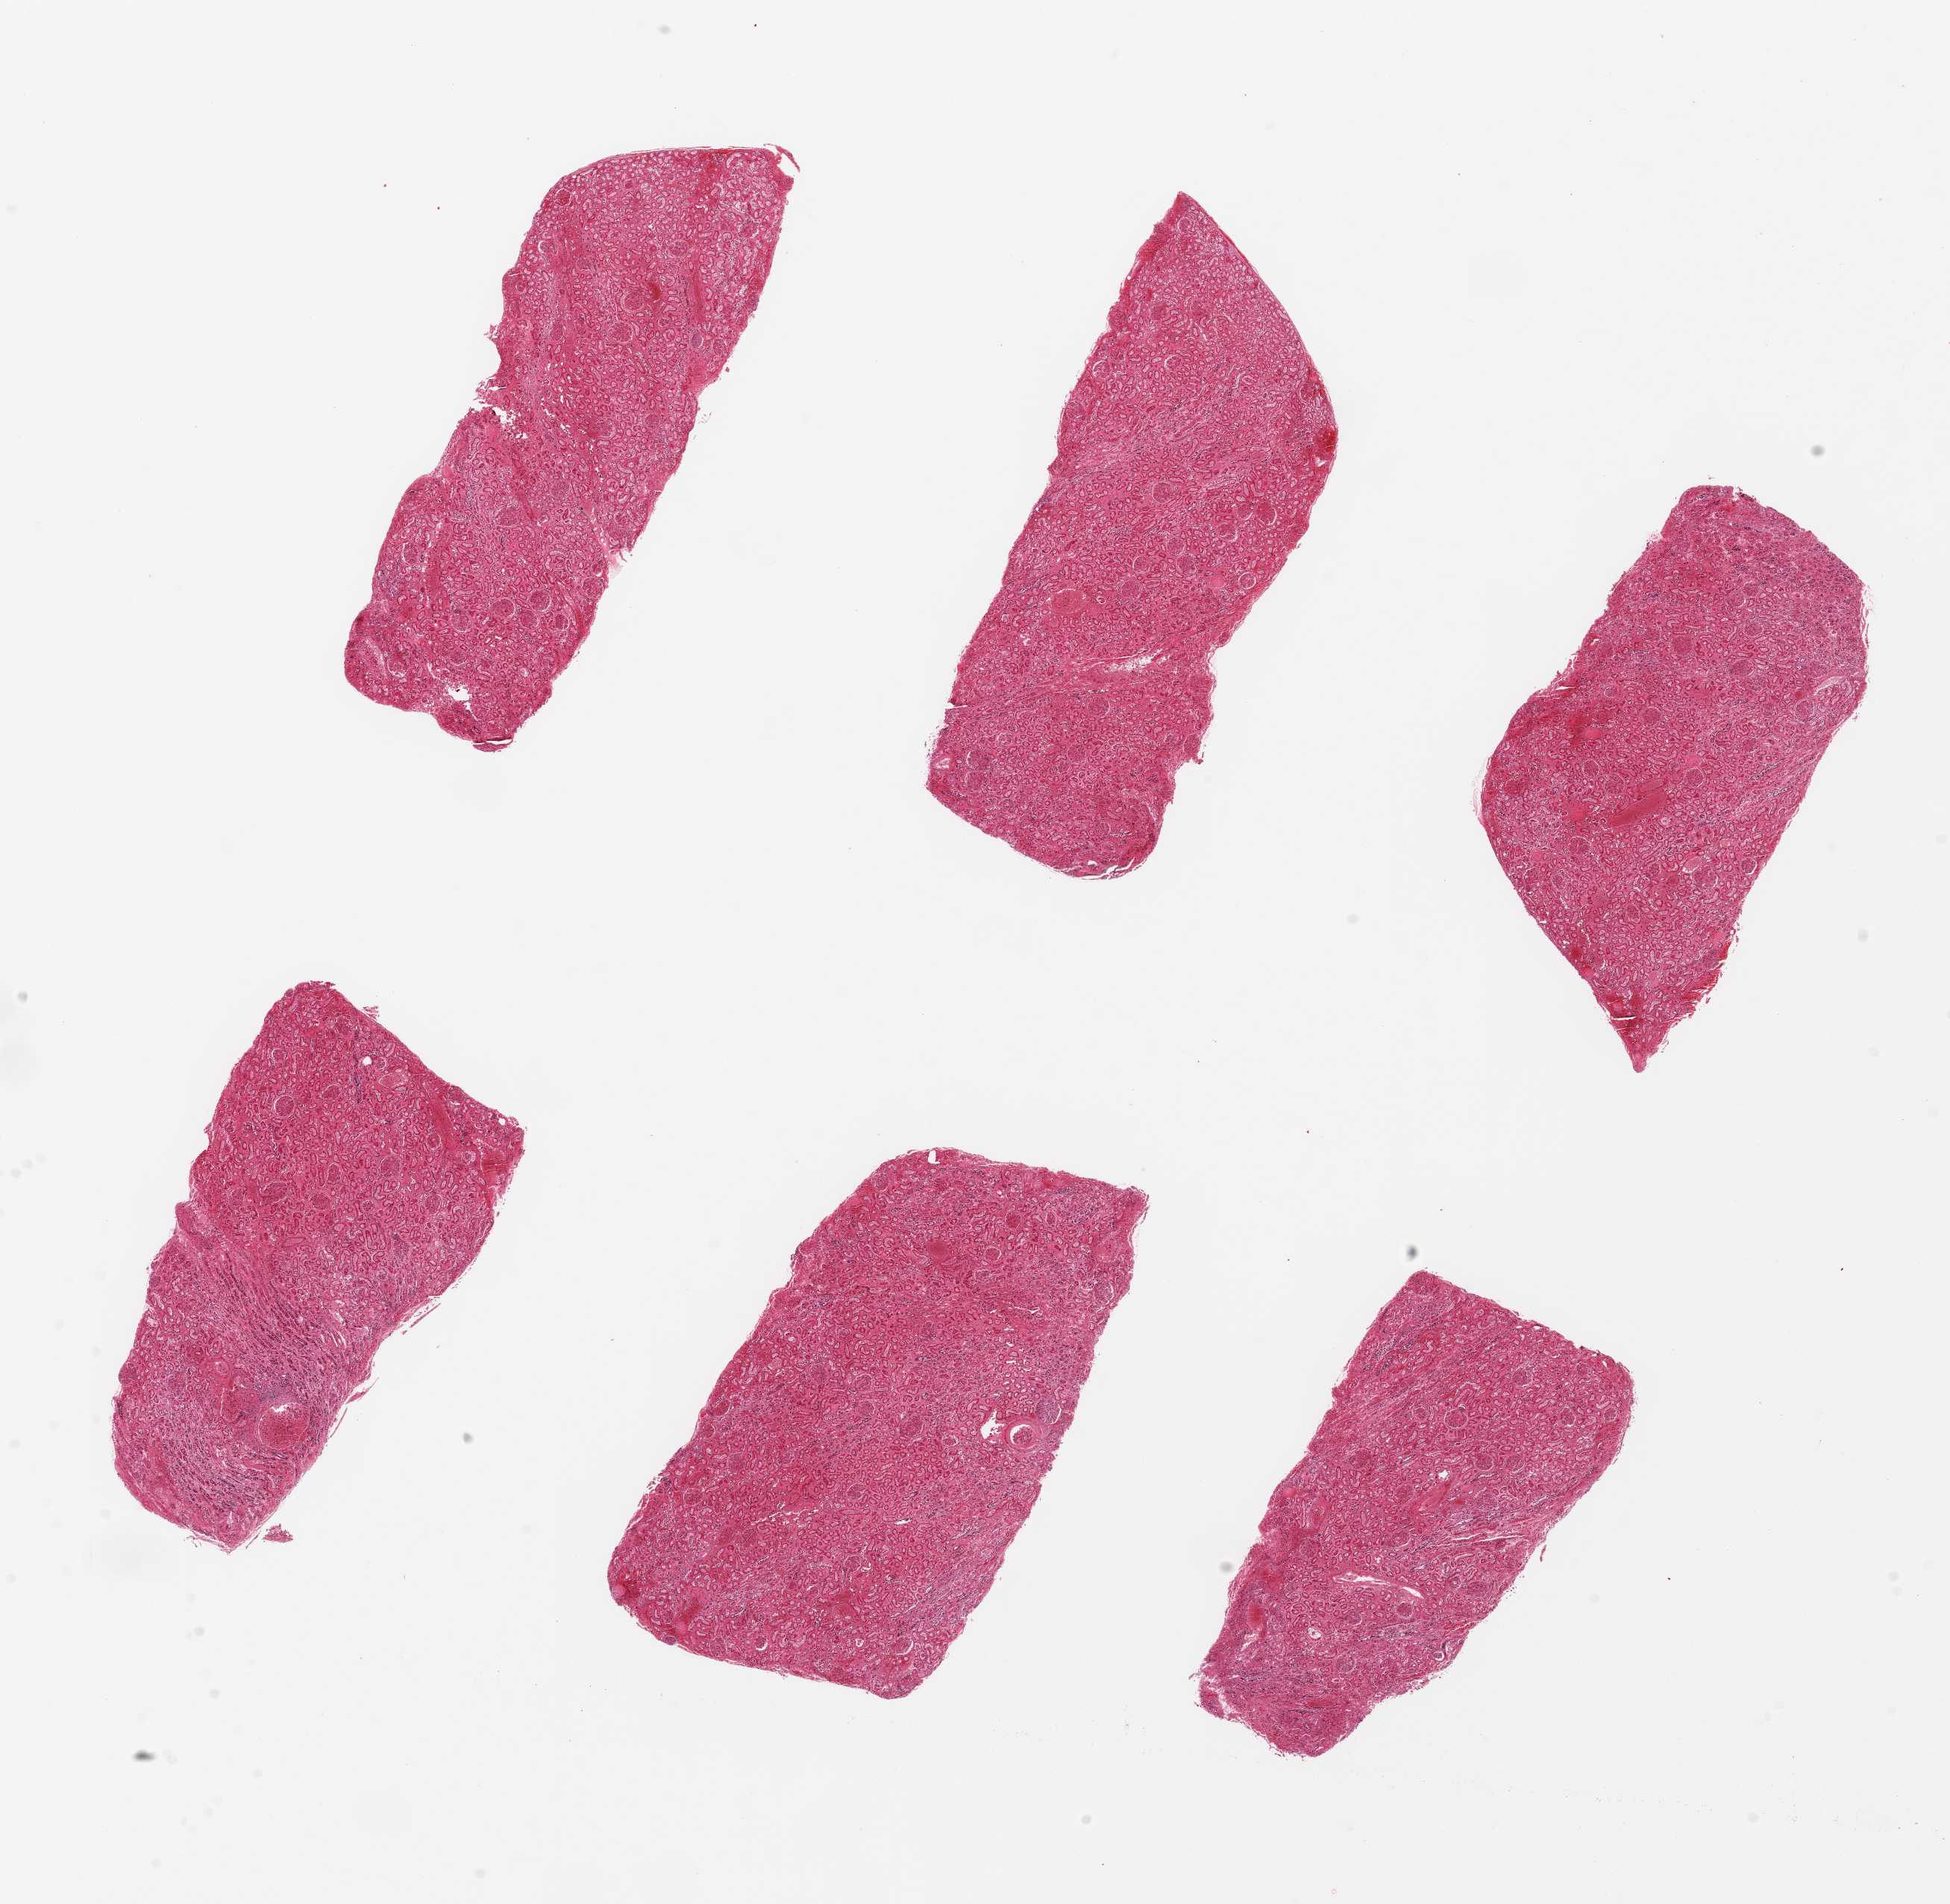
Haematoxylin and eosin whole-slide image, a low-resolution overview of the entire scanned area, about 20.7 x 20.2 mm (acquisition: 20x scan). PAXgene-fixed, paraffin-embedded tissue. Target tissue: renal cortex. Tissue donor sample. Donor: female.
* review note (as recorded): 6 pieces ~6x3mm